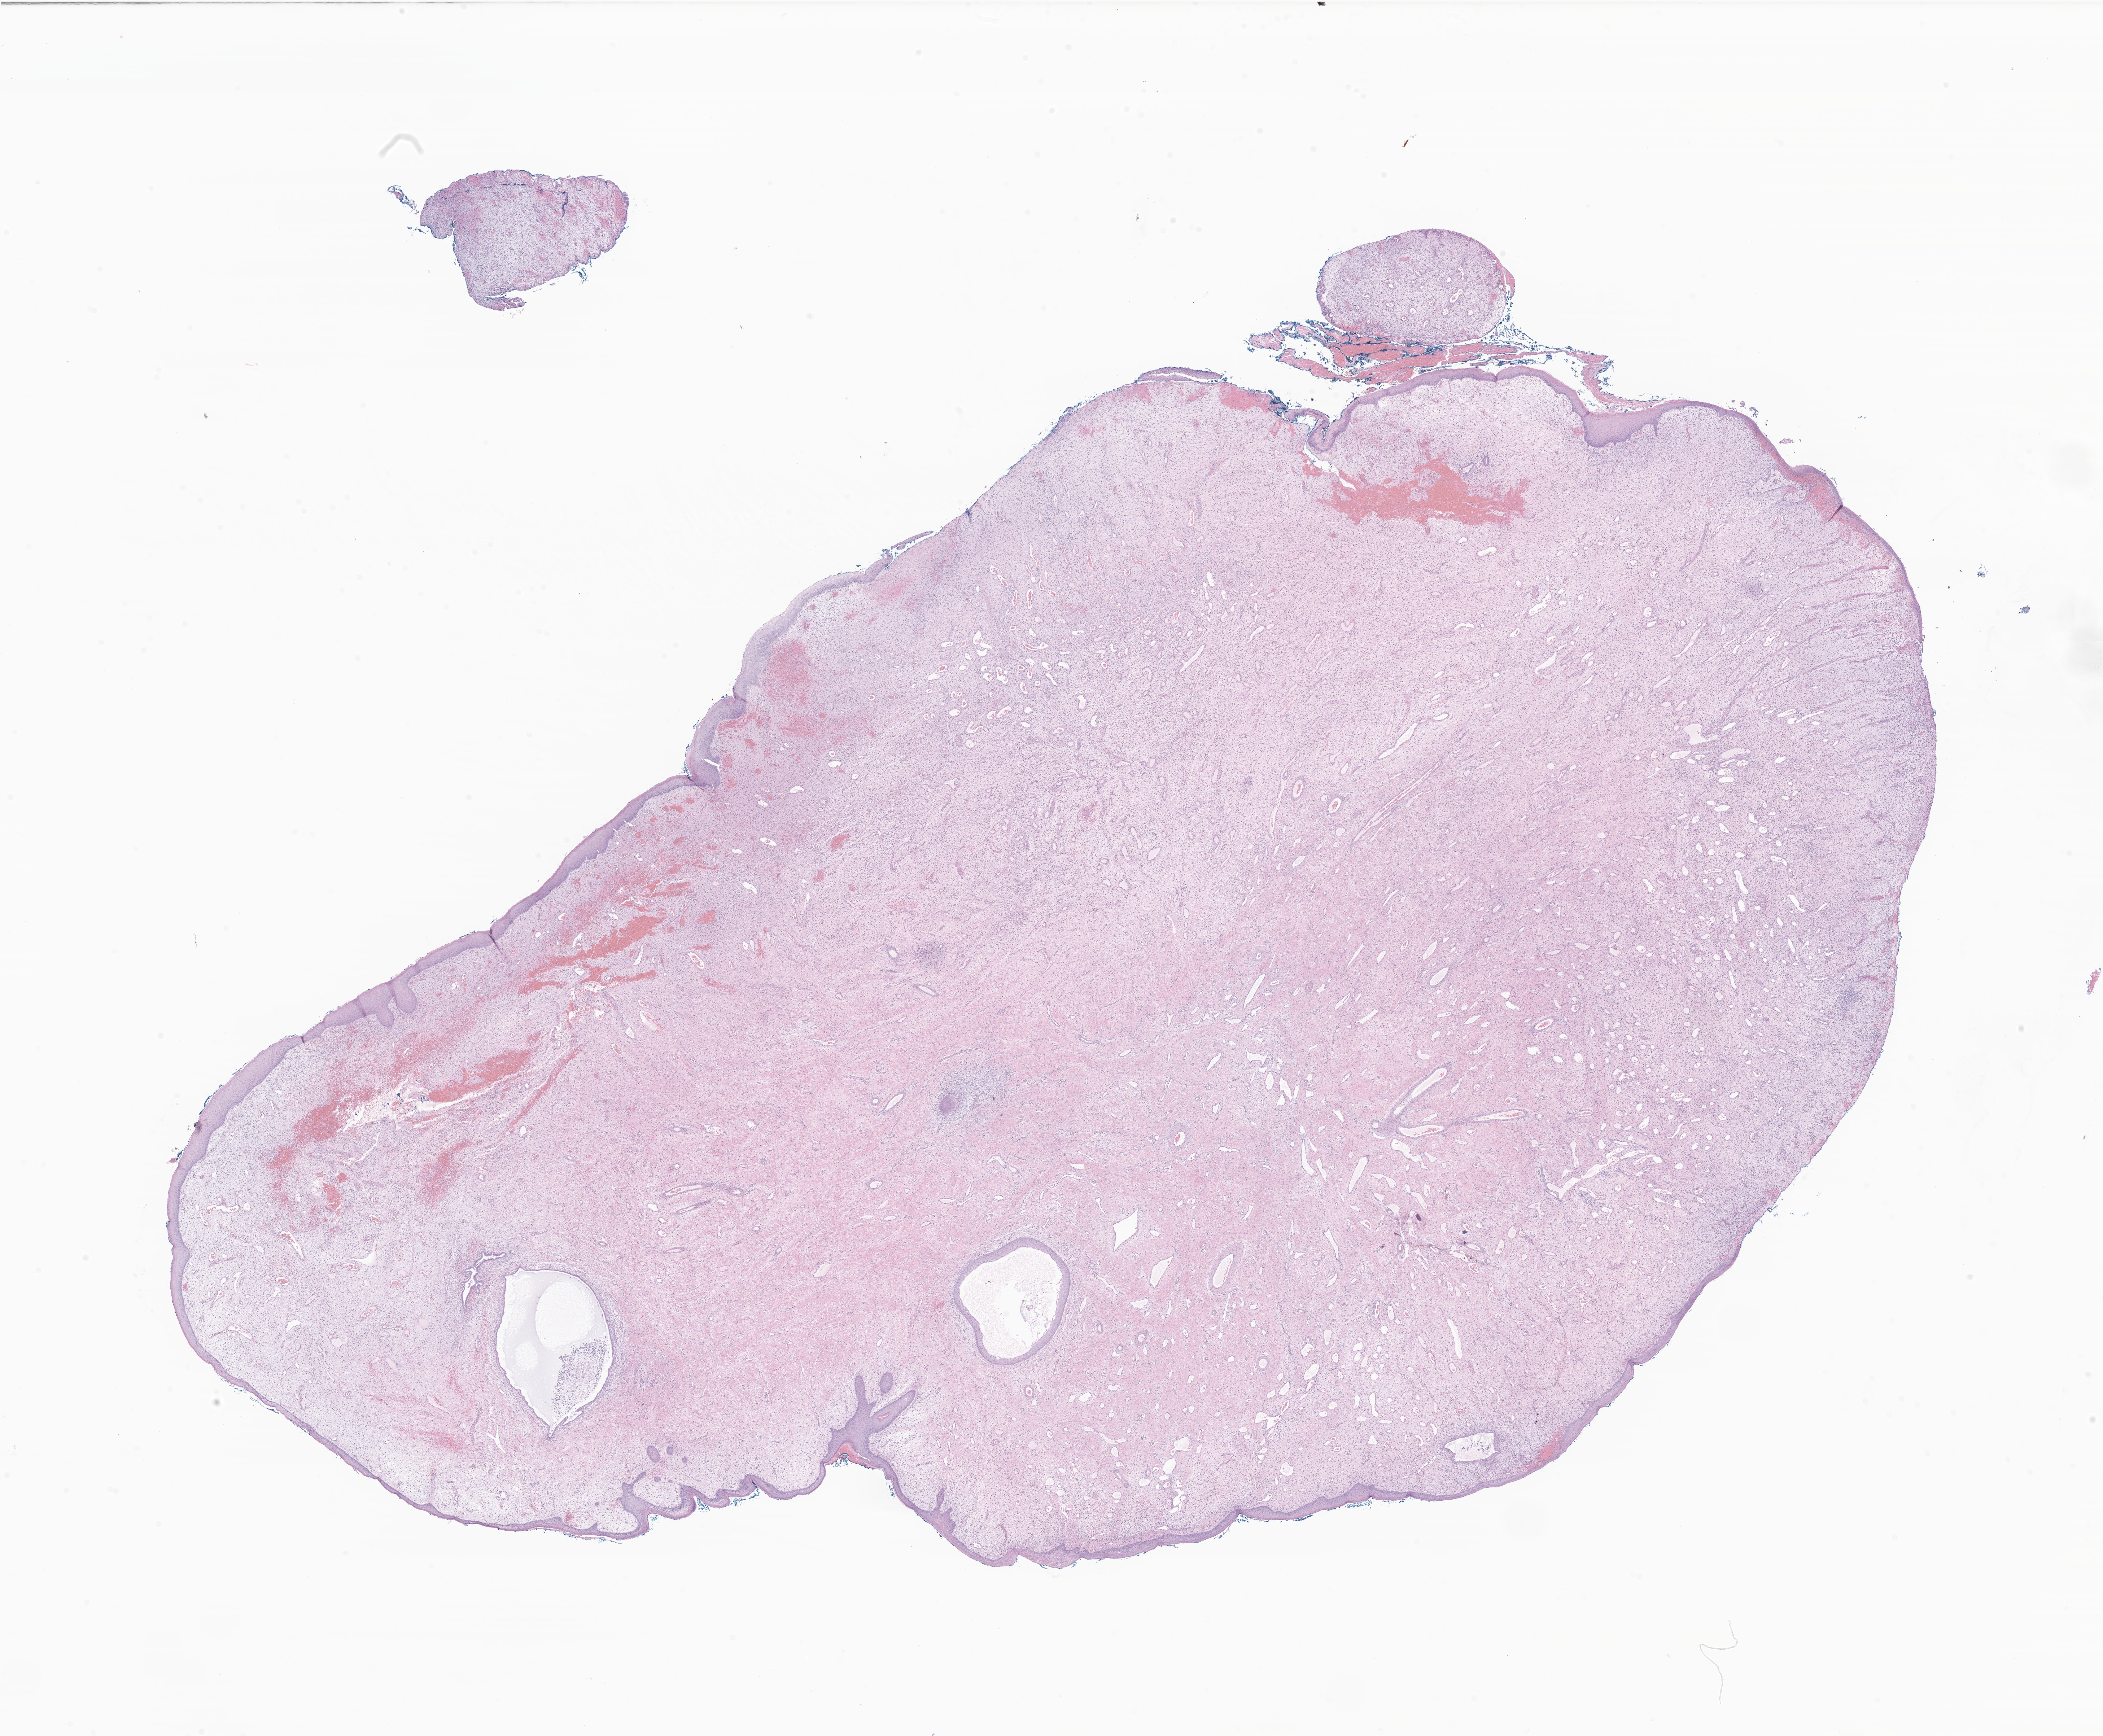
H&E whole-slide image of tumor tissue from the cervix uteri — a low-resolution overview of the entire scanned area, about 24.6 x 20.3 mm; formalin-fixed, paraffin-embedded (FFPE) tissue. Patient female; age 154 months (12 years 10 months).
Diagnosis: Embryonal rhabdomyosarcoma, NOS.